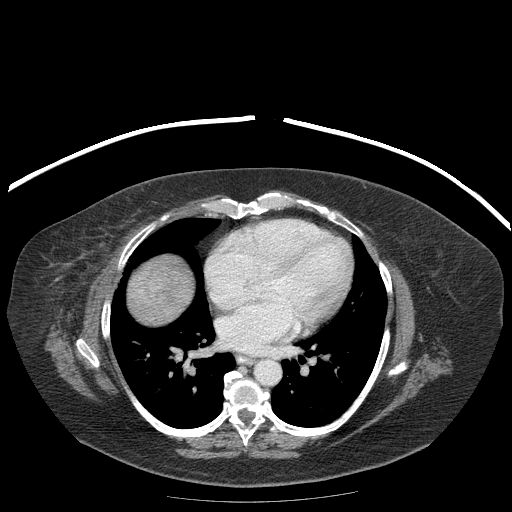
Contrast-enhanced abdominal CT (liver protocol), one axial slice. Position 187 of 204 along the scan axis. Reconstruction kernel STANDARD. 120 kVp. Soft-tissue window (W 400 / L 40 HU). 2.5 mm slice thickness. 512 × 512 image matrix, field of view 440 × 440 mm. Case-level facts recorded for this patient, not image findings: diagnosis: hepatocellular carcinoma (patient treated with transarterial chemoembolisation; whether this scan precedes or follows treatment is not stated here); TNM stage (as recorded): Stage-IIIB; Child-Pugh class: A; tumour nodularity: uninodular.
Annotated regions visible in this slice (semi-automatically segmented with operator editing):
- liver parenchyma outside the tumour (the mass and vessels are separate outlines, so this box may not span the whole liver): bounding box (x1, y1, x2, y2) in pixels: (128, 254, 192, 324)
- mass: (146, 260, 189, 312)